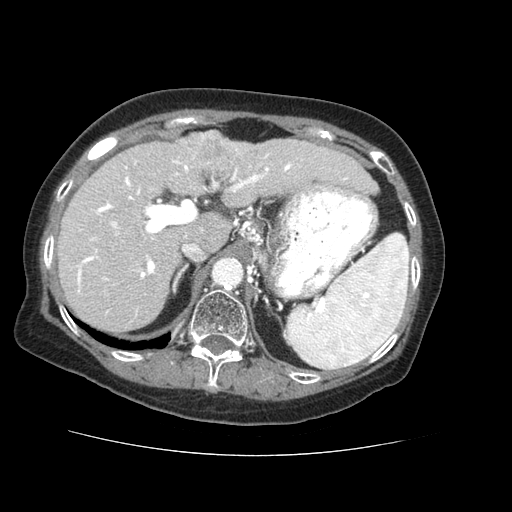
Contrast-enhanced abdominal CT (liver protocol), one axial slice; slice 41 of 73 in the series (ordered by position); reconstruction kernel STANDARD; 120 kVp; soft-tissue window (W 400 / L 40 HU); 2.5 mm slice thickness; 512 × 512 image matrix. Case-level facts recorded for this patient, not image findings: diagnosis: hepatocellular carcinoma (patient treated with transarterial chemoembolisation; whether this scan precedes or follows treatment is not stated here); TNM stage (as recorded): Stage-IVB; Child-Pugh class: A.
Annotated regions visible in this slice (semi-automatic segmentation, software-assisted and operator-edited):
- liver parenchyma outside the tumour (the mass and vessels are separate outlines, so this box may not span the whole liver): bounding box [x1, y1, x2, y2] px = [56, 132, 378, 332]
- mass: [166, 129, 238, 171]
- liver vessels: [77, 152, 348, 313]